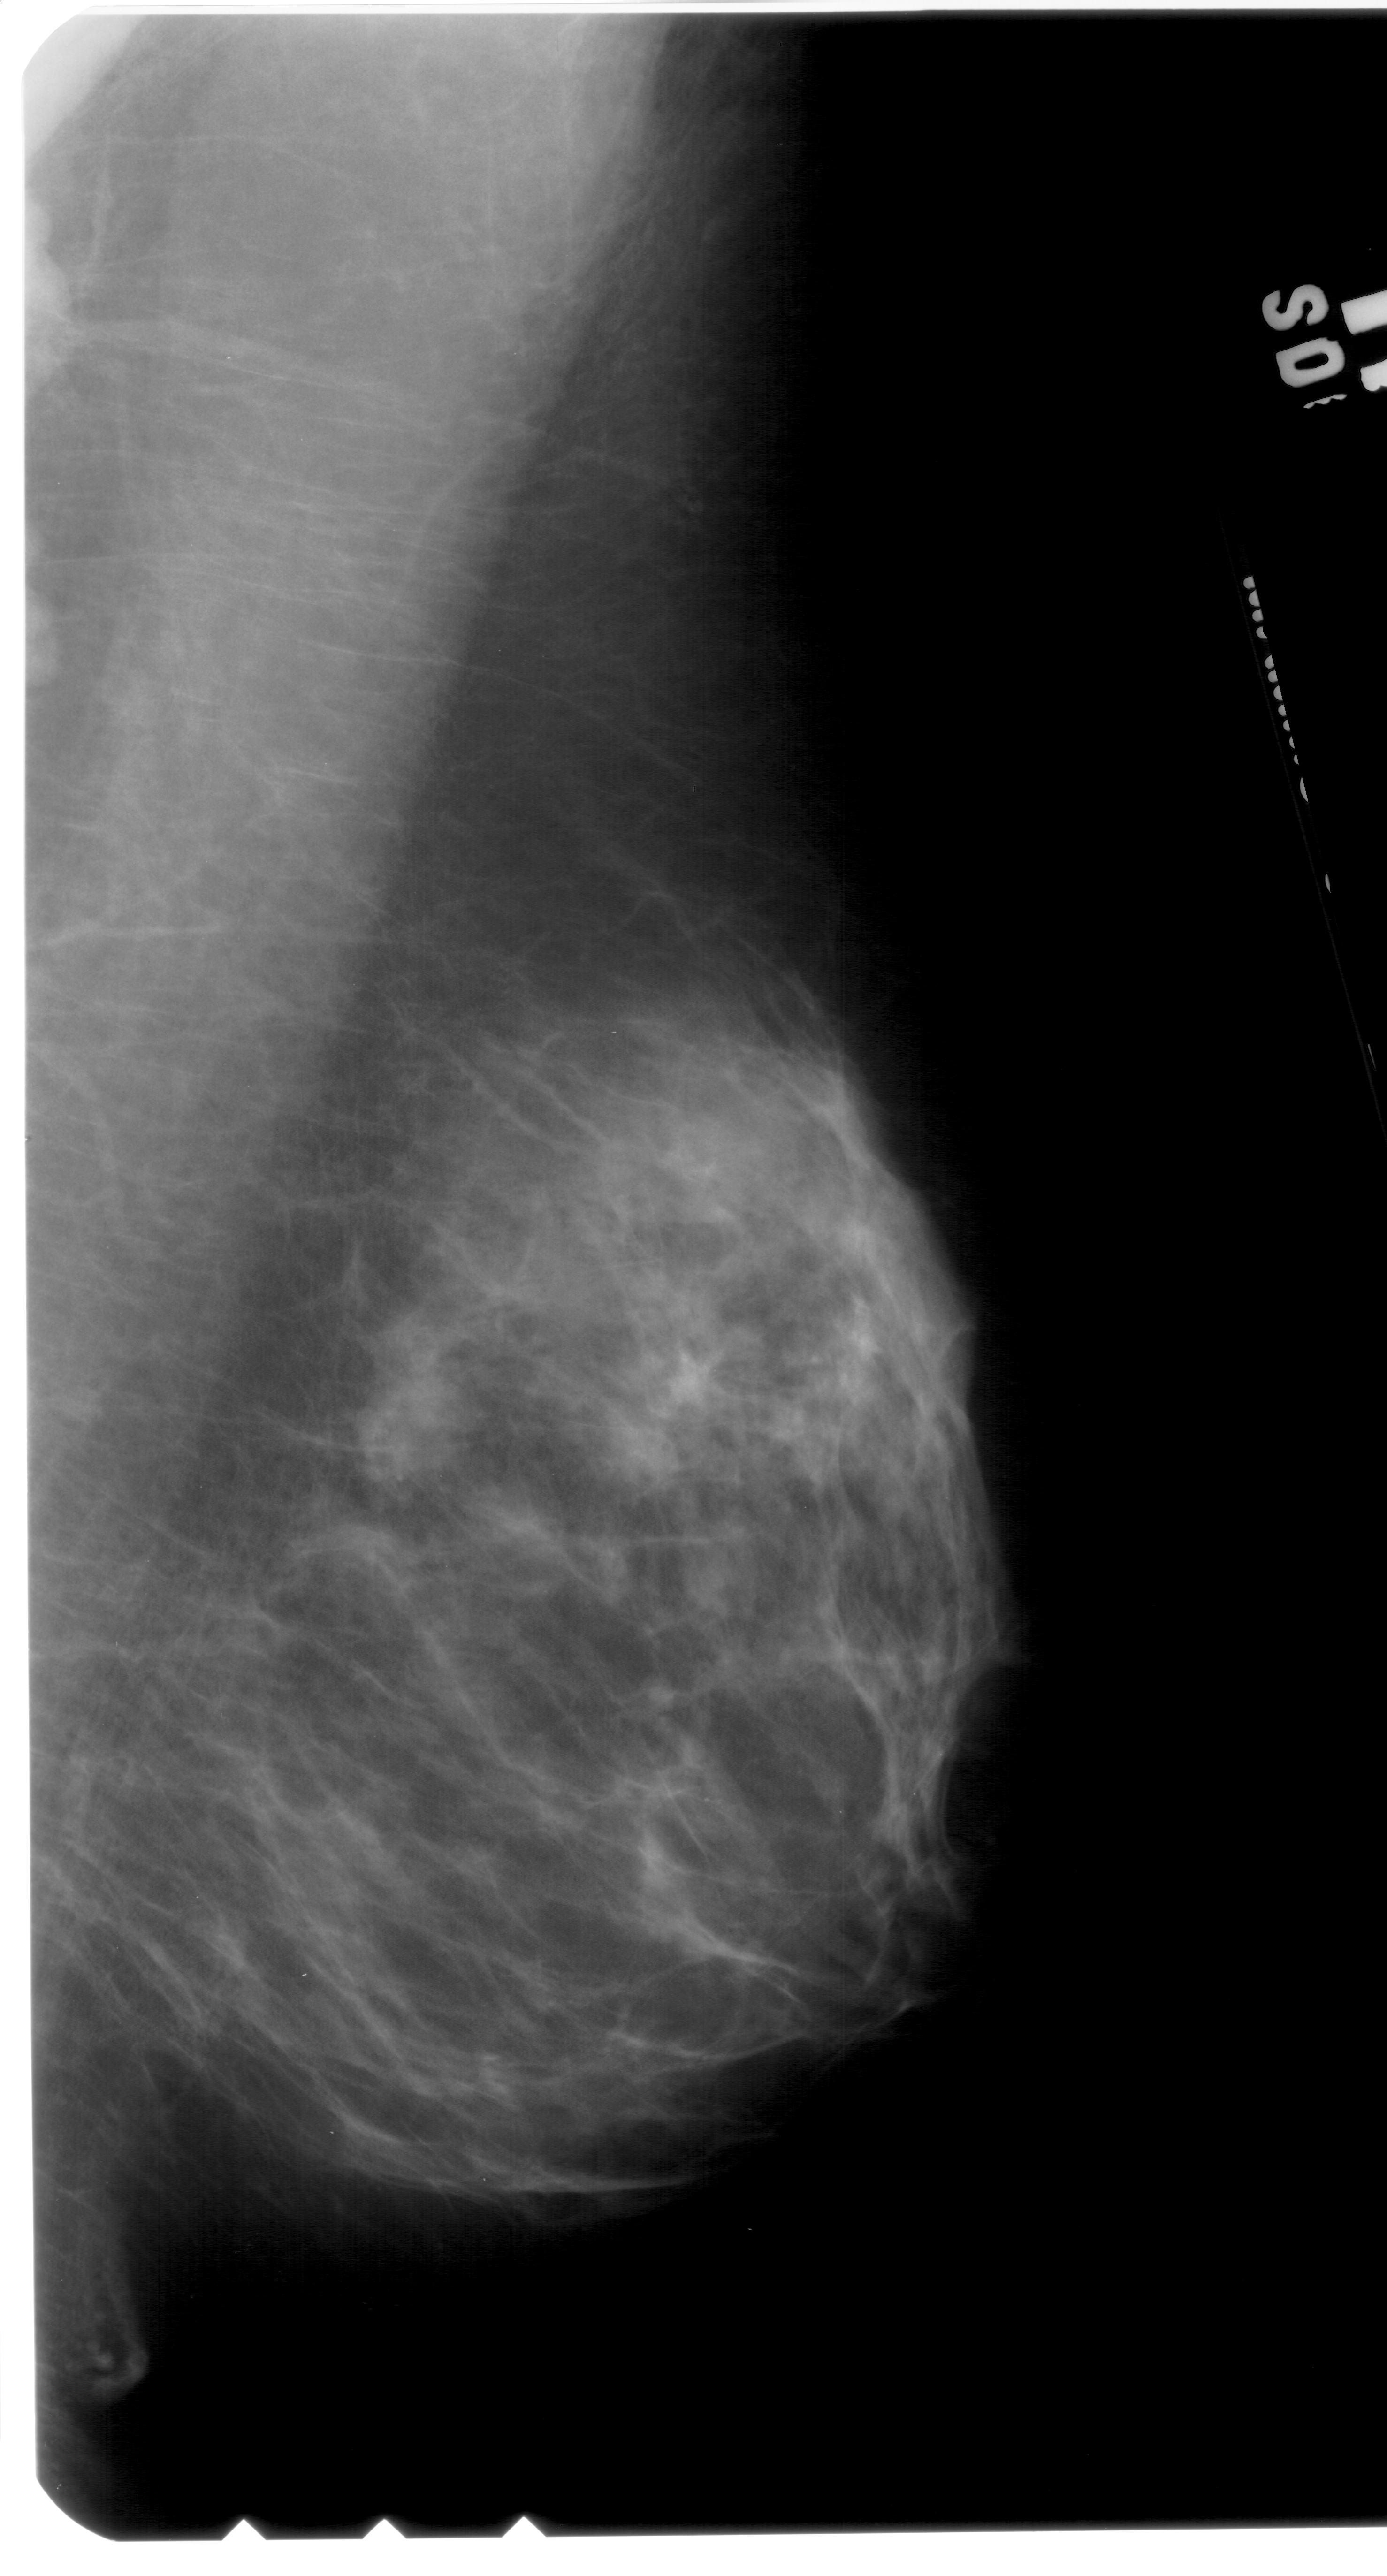
Scanned film-screen mammogram. Right breast. Mediolateral oblique (MLO) view. Breast composition: almost entirely fatty (BI-RADS density category 1 of 4). 1387 × 2576 image matrix.
Expert-marked regions of interest on this film, with their recorded descriptors:
- calcifications, morphology pleomorphic, distribution clustered; BI-RADS assessment category 4; subtlety rating 1 on a 1 (subtle) to 5 (obvious) scale; pathology (as recorded): benign: bounding box <652,1759,764,1842> (left, top, right, bottom; pixels)